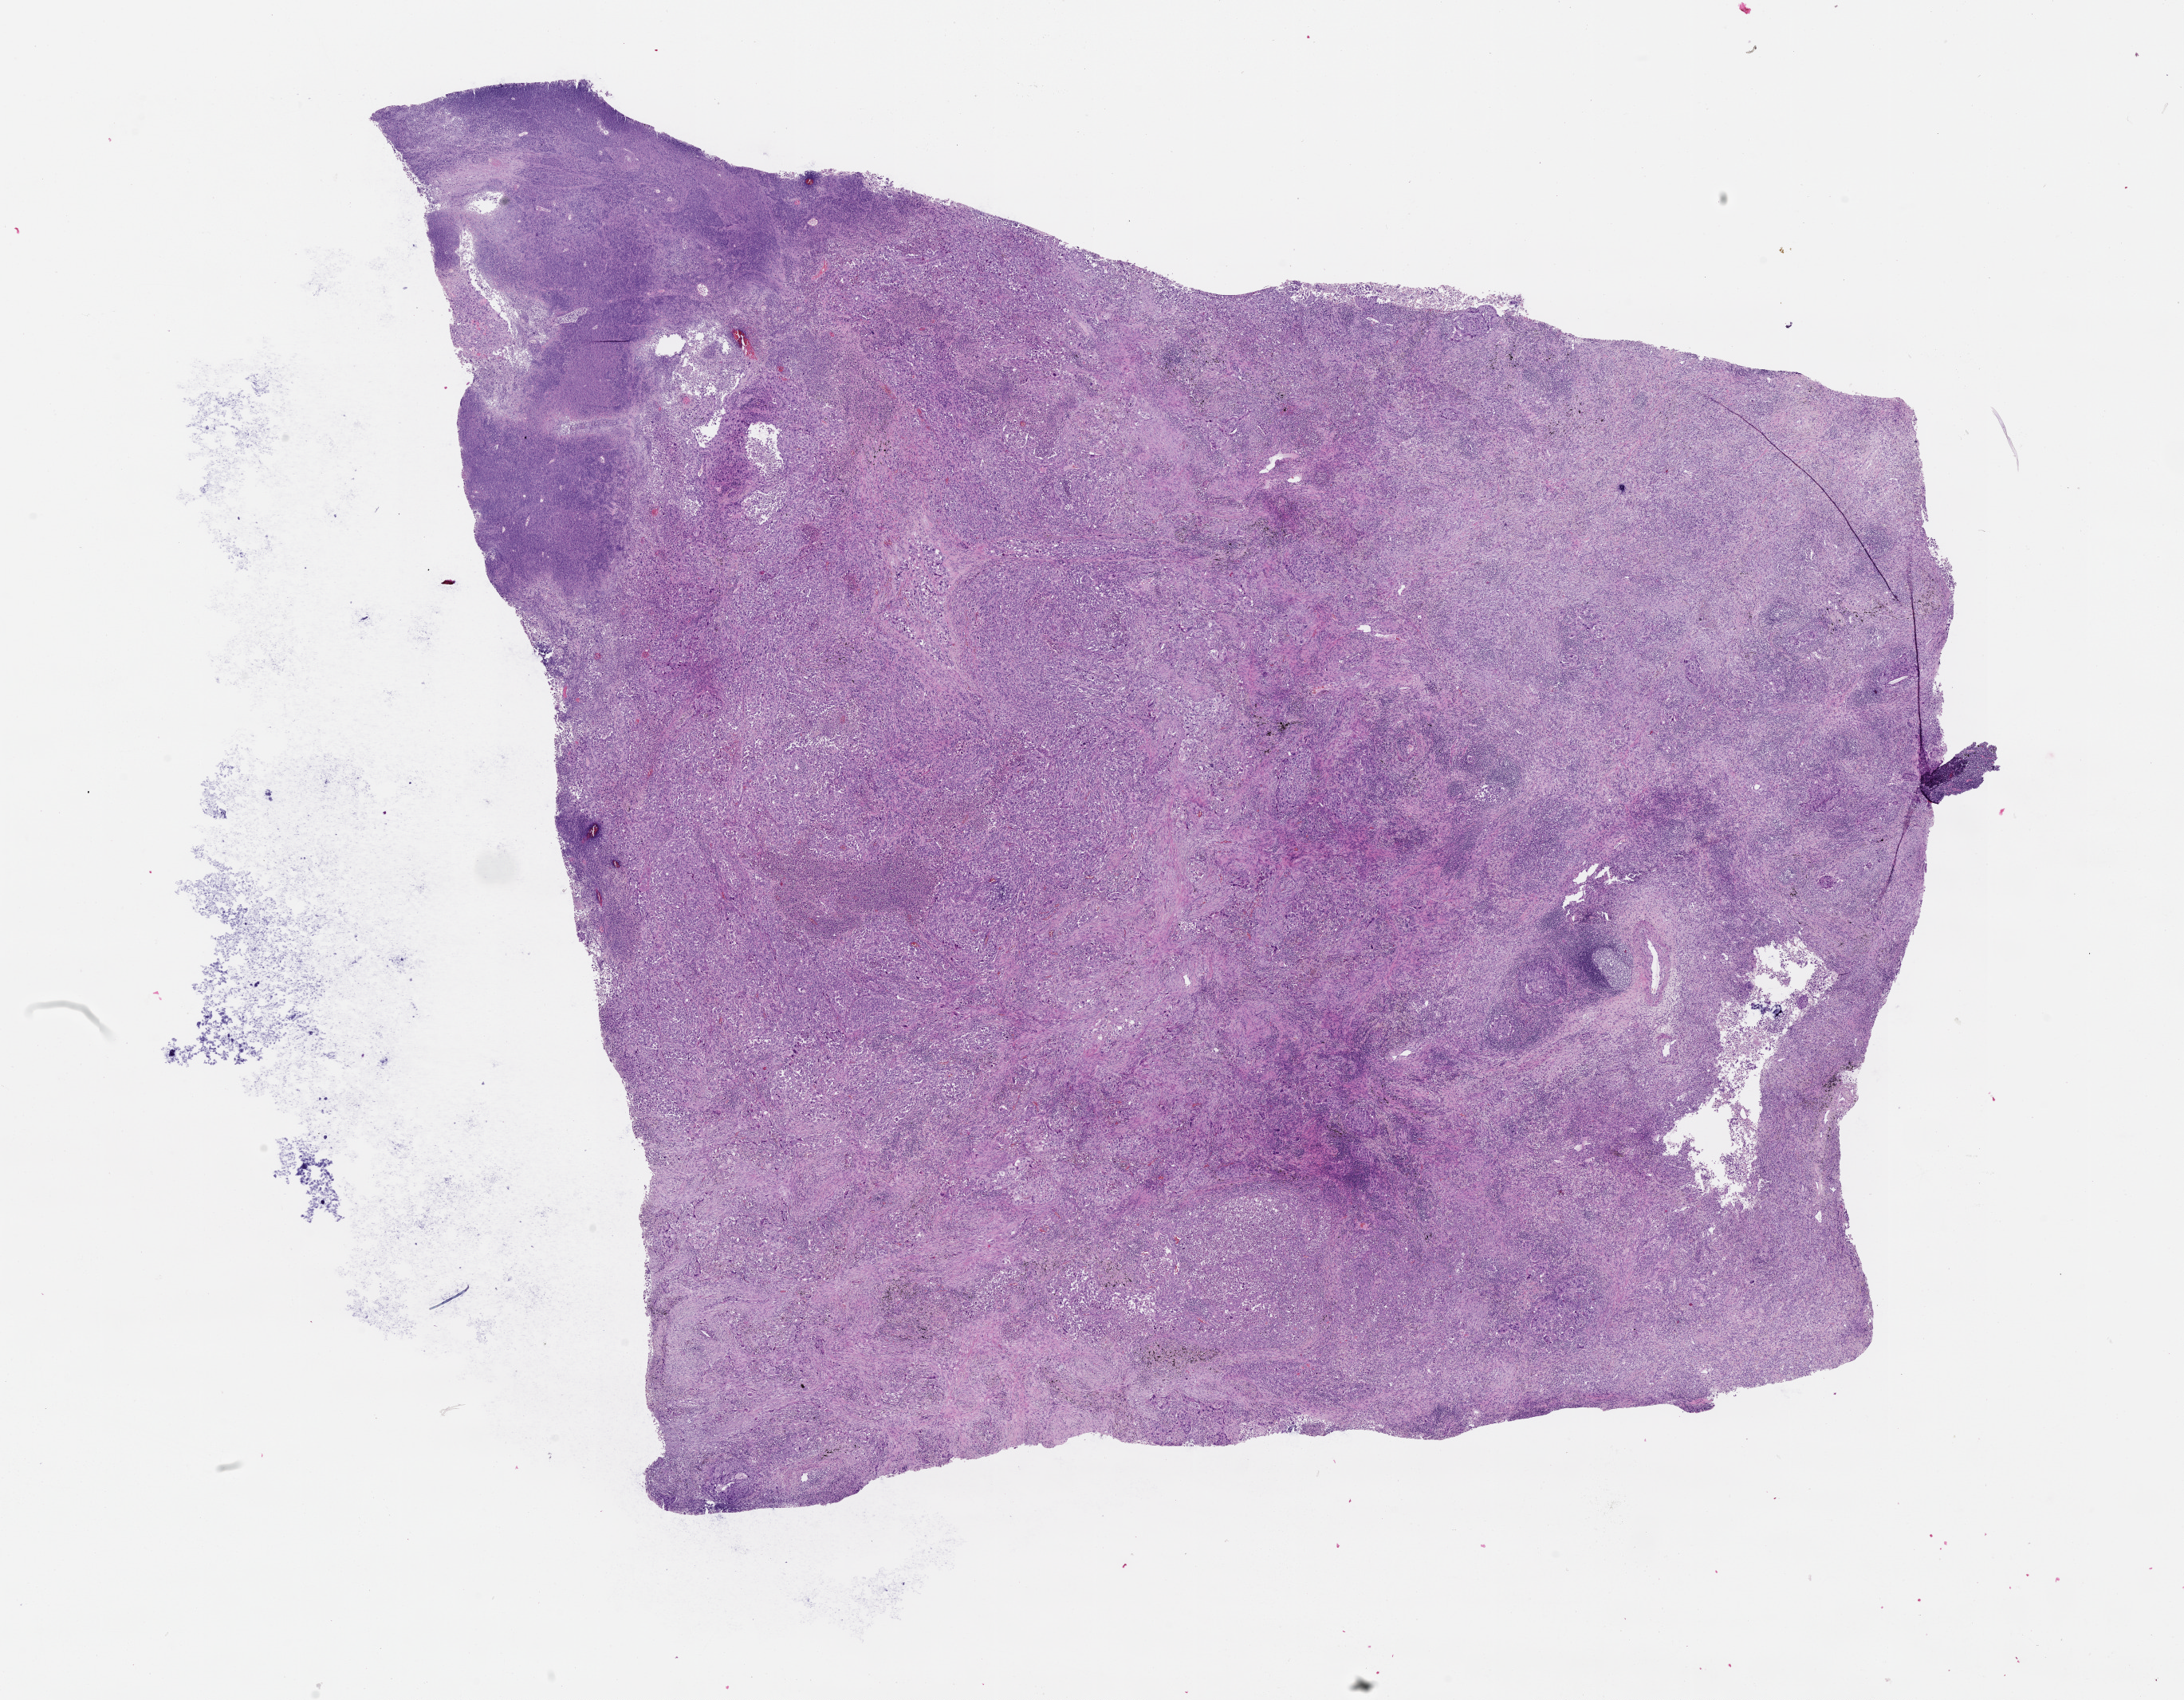
Hematoxylin and eosin (H&E) stained whole-slide image, low-resolution overview of the scanned area, about 22.0 x 17.2 mm (from a 20x scan), lung, tissue type not recorded.
Patient diagnosis (cohort enrolment): squamous cell carcinoma (lung).